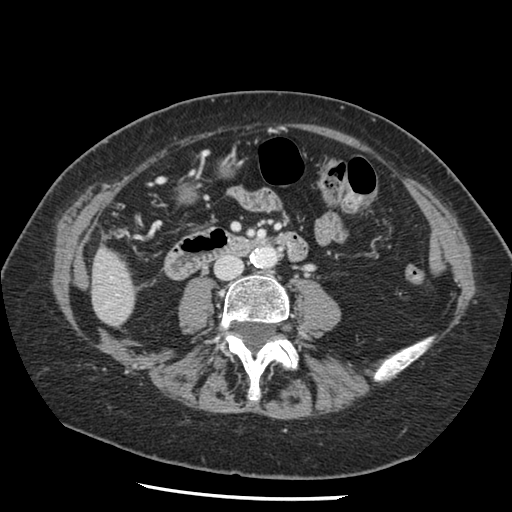
Contrast-enhanced abdominal CT, one axial slice; slice 22 of 148 in the series (ordered by position); reconstruction kernel STANDARD; 120 kVp; intravenous contrast given; soft-tissue window (W 400 / L 40 HU); 2.5 mm slice thickness; 512 × 512 image matrix, field of view 330 × 330 mm. Female patient, age 85 years. Case-level facts recorded for this patient, not image findings: diagnosis: colorectal cancer liver metastases, imaged before liver resection; multiple liver metastases: no; largest metastasis: 0.9 cm.
Structures marked on this image (manually delineated by an expert):
- liver: box from (x=93, y=251) to (x=135, y=325) px
- planned liver remnant (the part of the liver to remain after resection): (x=93, y=251)–(x=135, y=324)